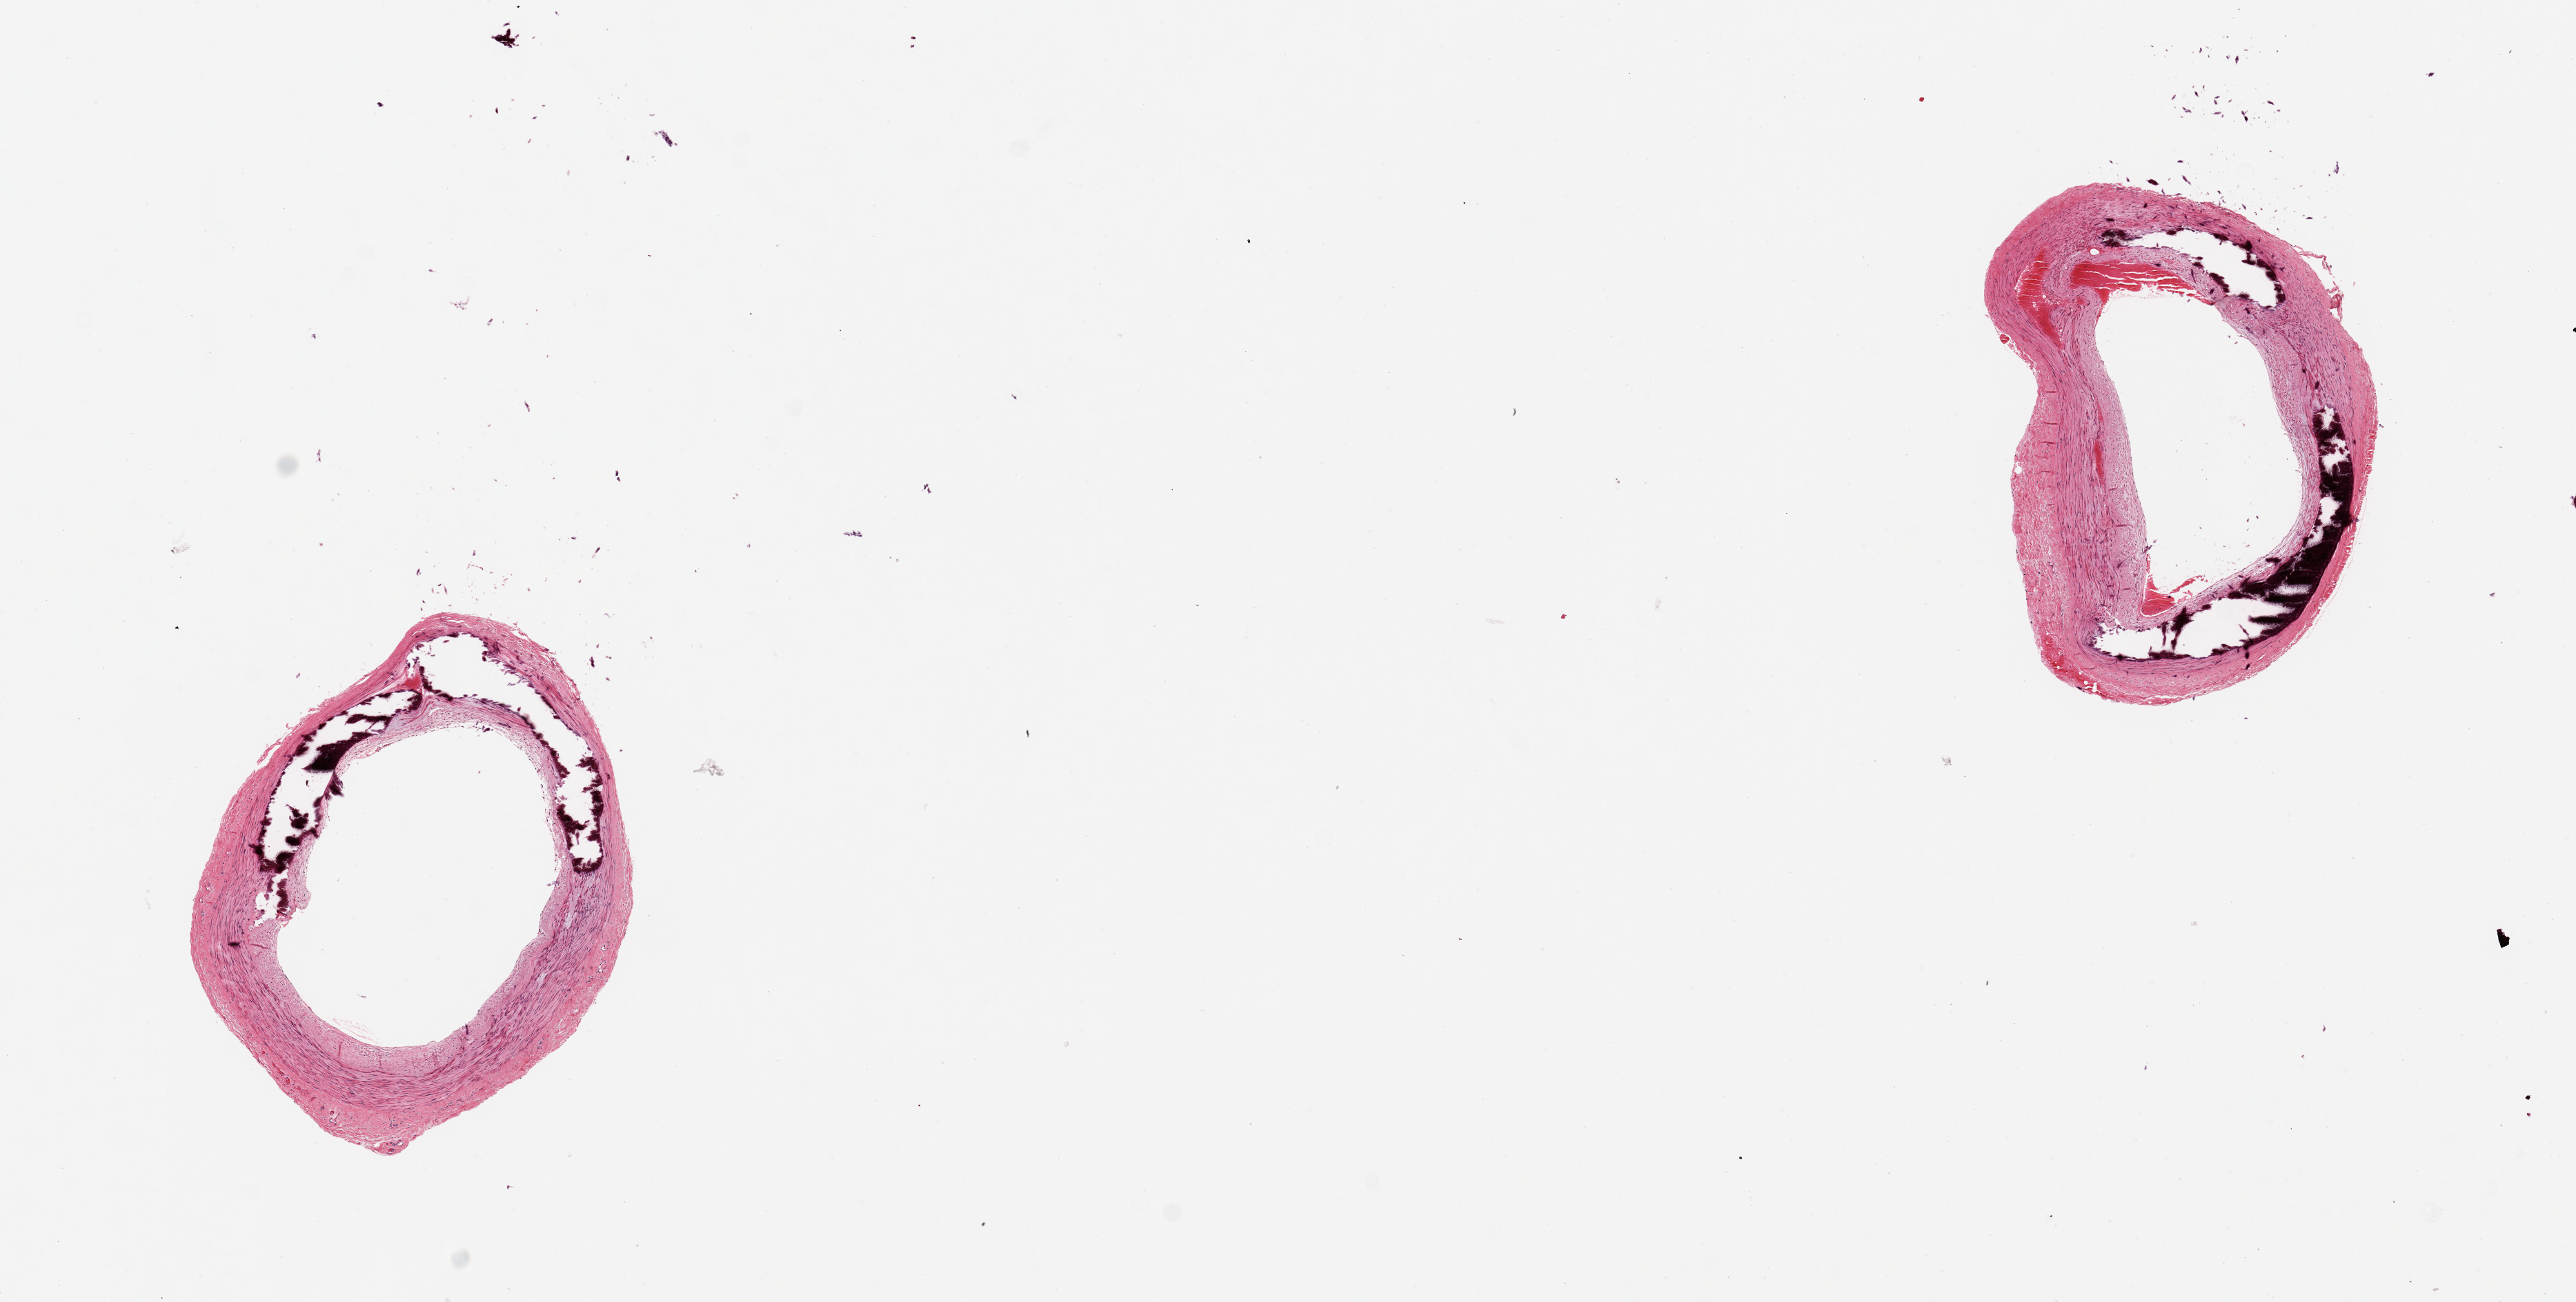
Whole-slide image, hematoxylin and eosin (H&E) stain, brightfield, a low-resolution overview of the entire scanned area, about 14.8 x 7.5 mm (slide scanned at 20x), PAXgene-fixed paraffin-embedded (PFPE) section, section of tibial artery (target tissue), donor tissue sample. Male donor.
Review note (as recorded): 2 pieces, Monckeberg's medial sclerosis present in both.